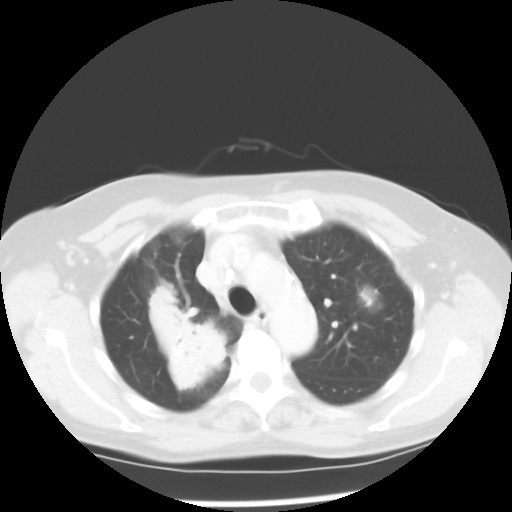
Chest CT, one axial slice; slice 38 of 52 in the series (ordered by position); reconstruction kernel STANDARD; 100 kVp; lung window (W 1500 / L -600 HU); 512 × 512 image matrix. Female patient, age 60 years. From the clinical record (not read from this slice): clinical TNM (as recorded): T2 N1 M1a.
Outlined on this slice (rectangle marked by the reading radiologist):
- lung tumour (recorded histology: adenocarcinoma): bounding box <137,275,235,396> (left, top, right, bottom; pixels)